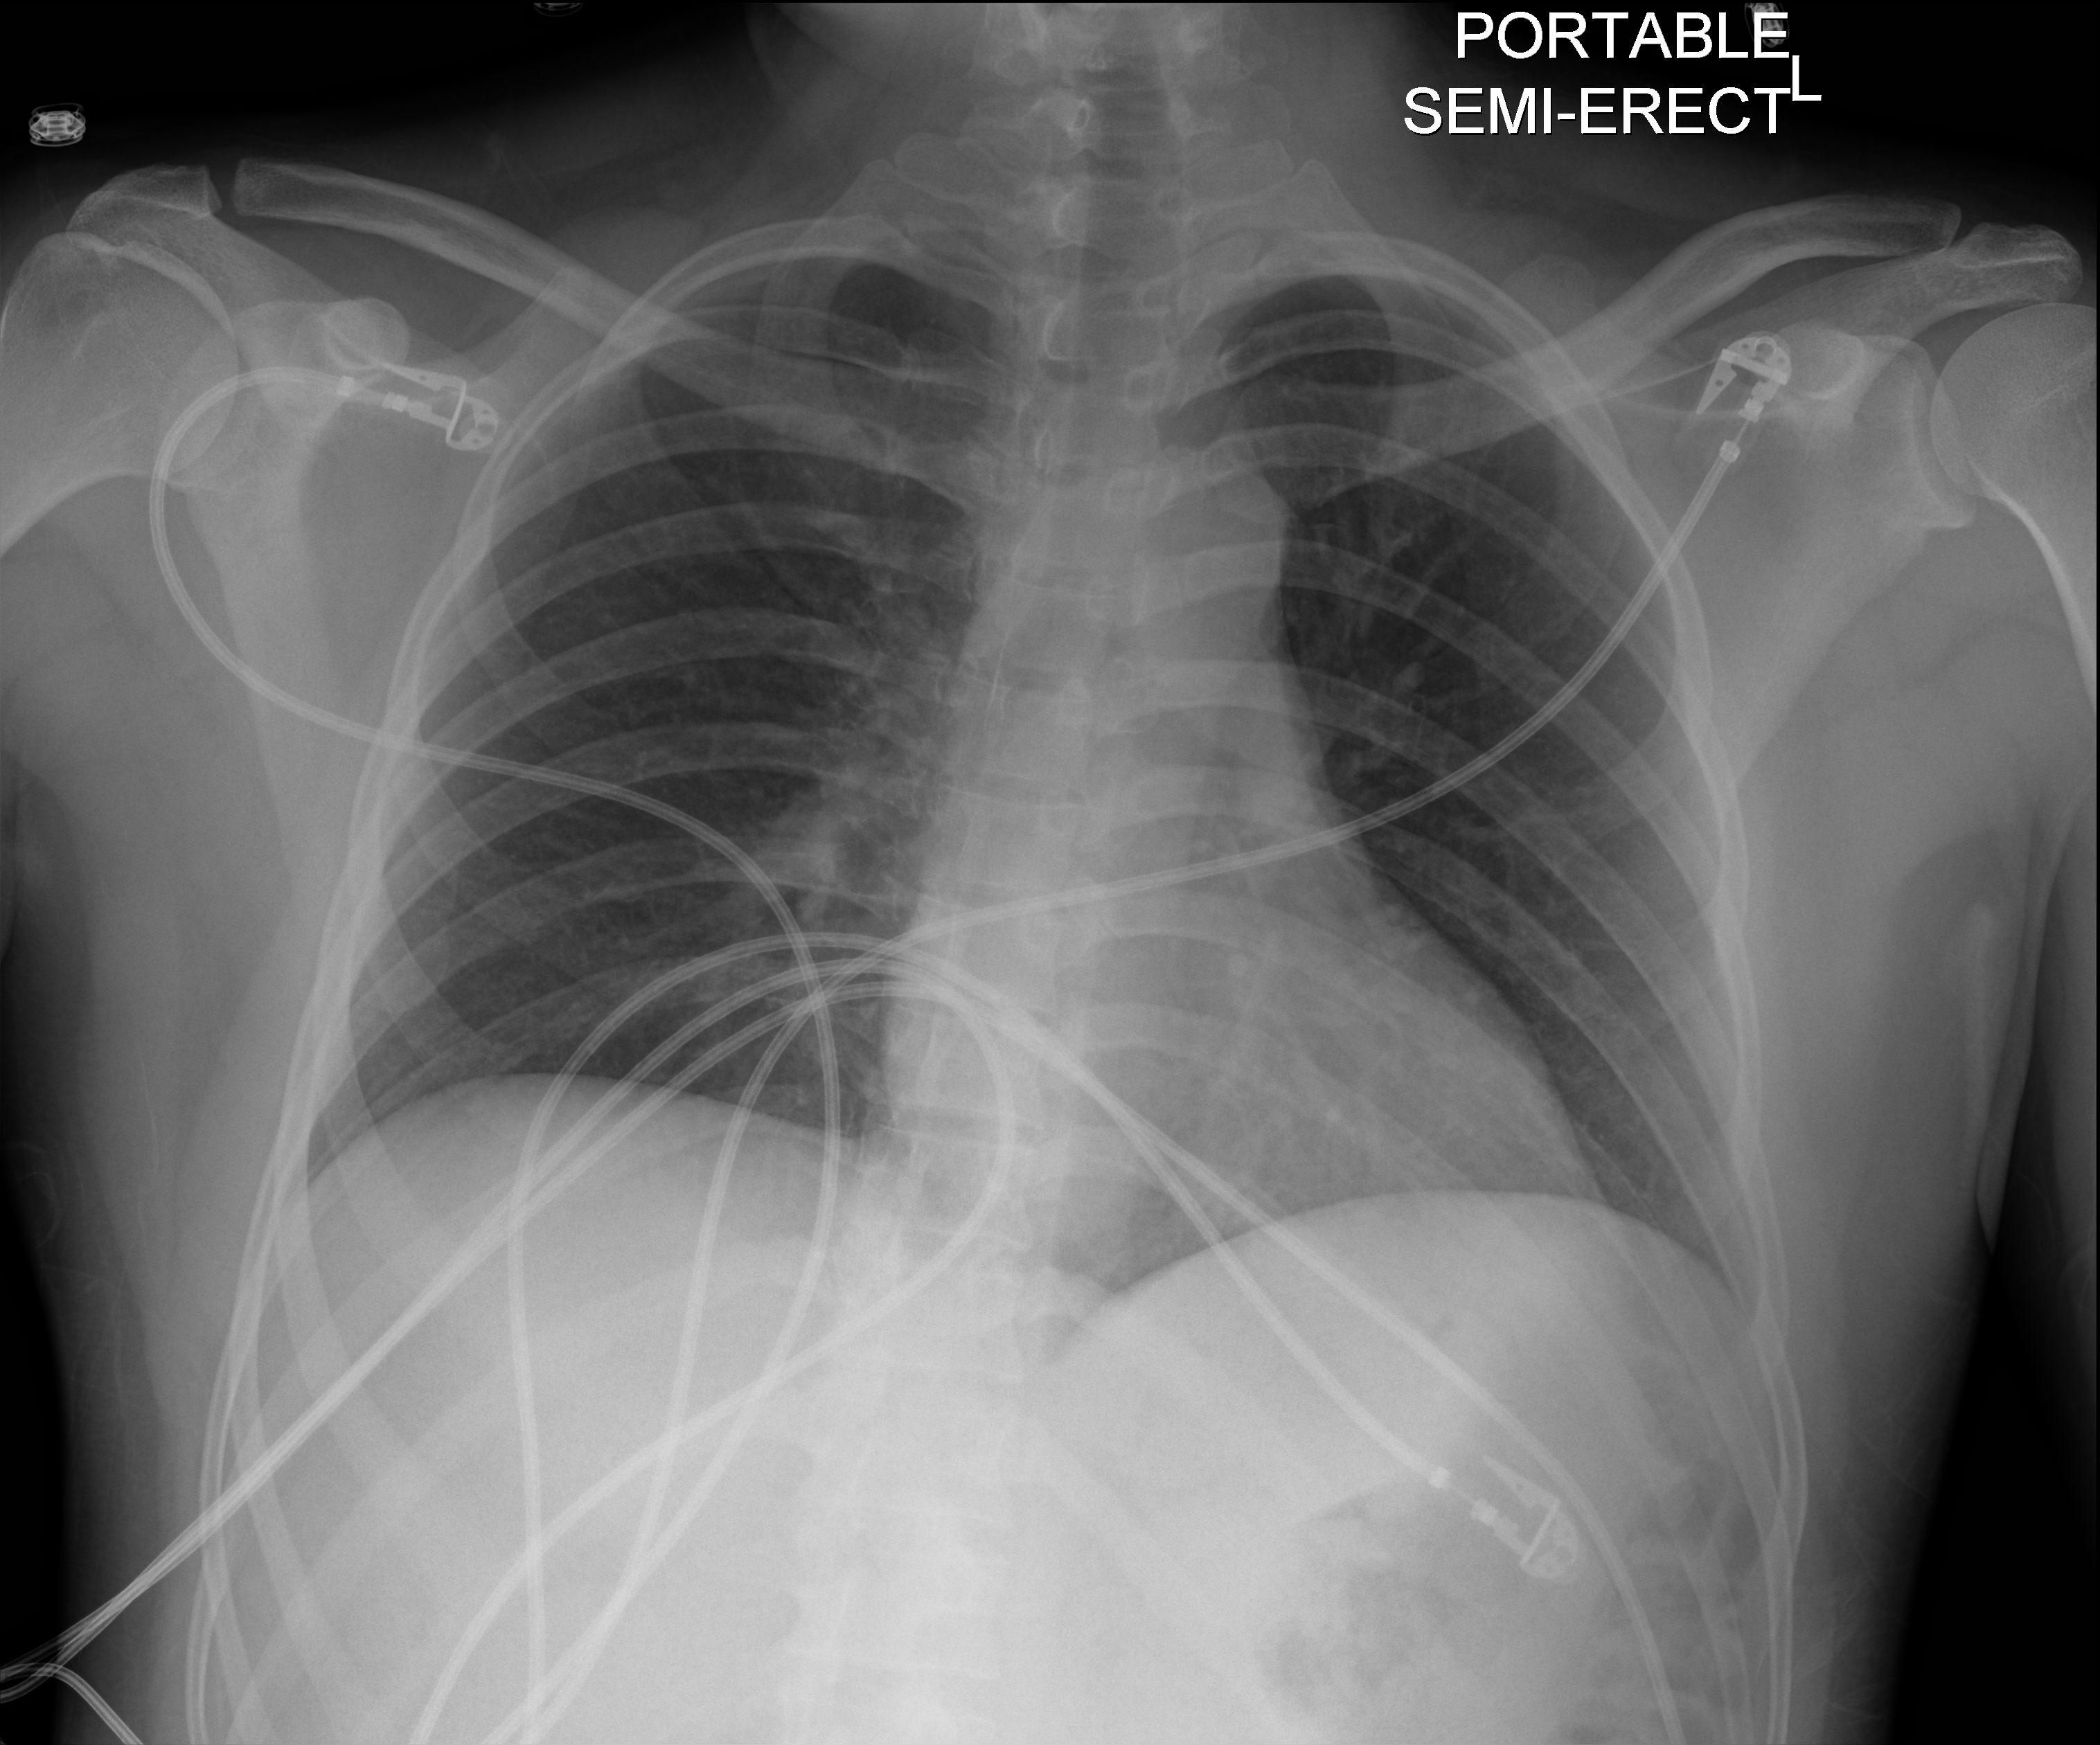
Bedside chest radiograph (digital radiography), anteroposterior (AP) projection. Male patient hospitalised with COVID-19, age 18–59 years.
From the hospital-stay record, not from the radiograph (when in the stay this image was taken is not recorded): length of hospital stay: 7 days; mechanically ventilated during this hospital stay: no; admitted to intensive care during this hospital stay: no.